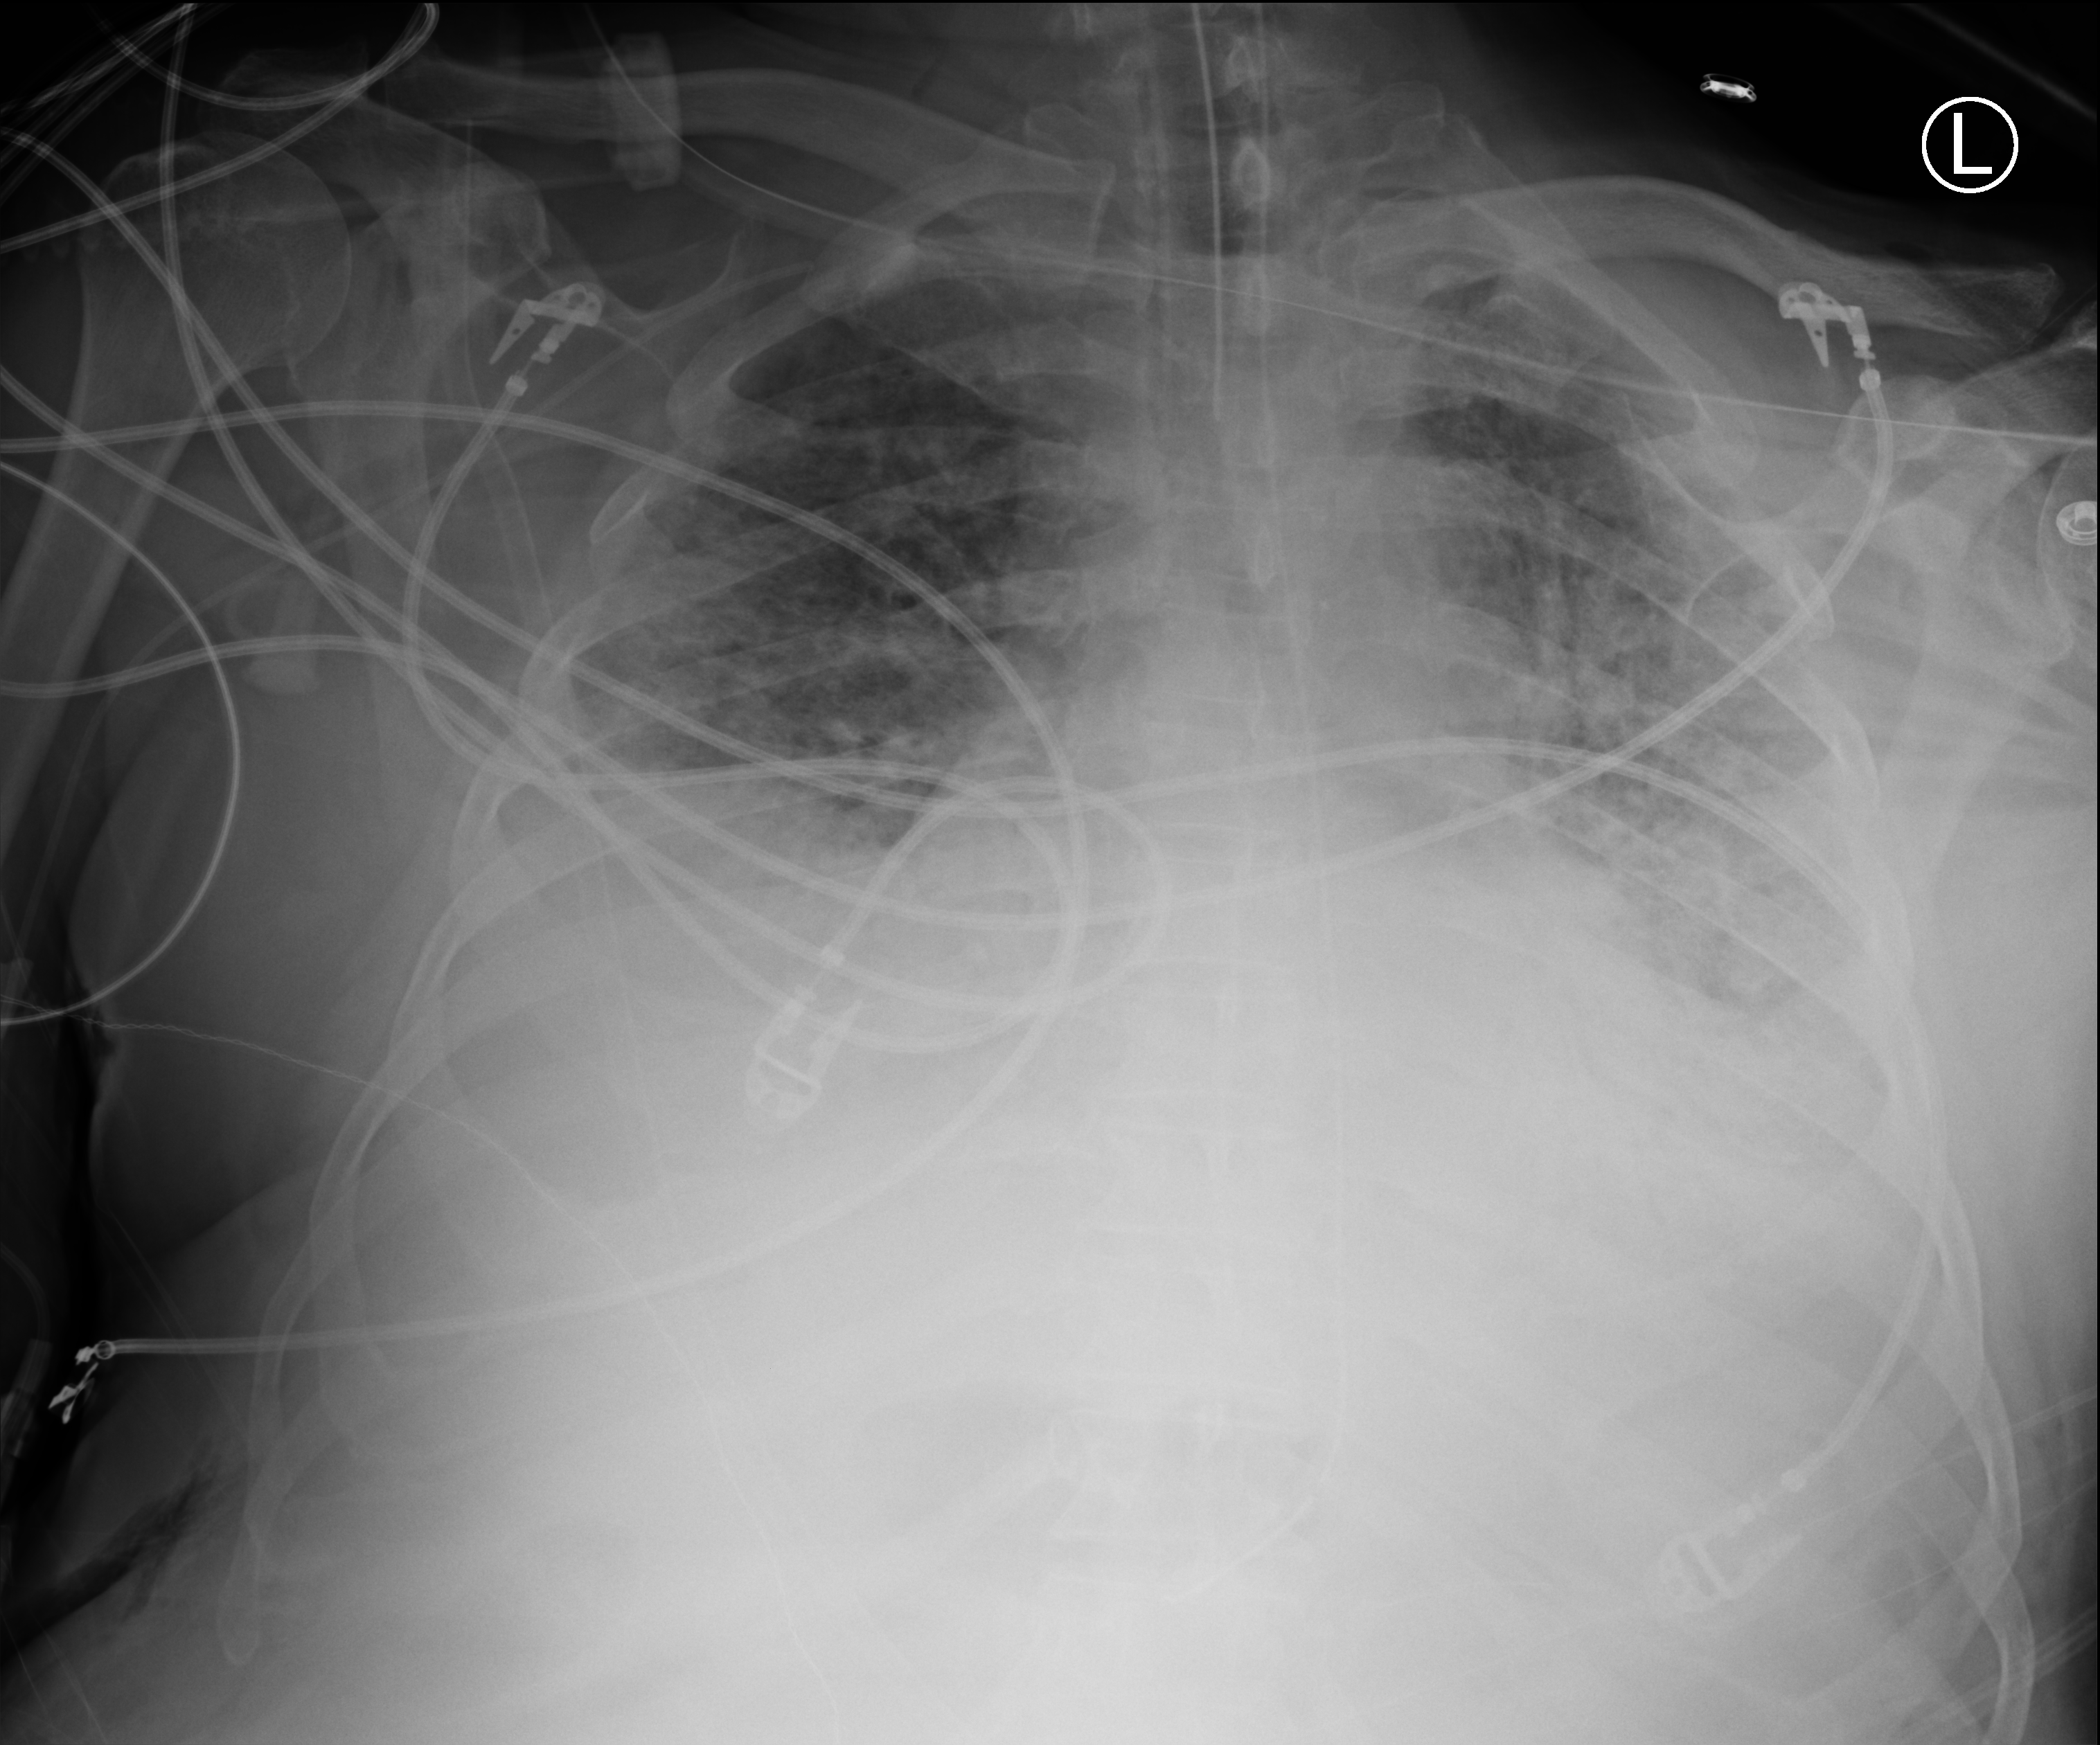
Portable chest radiograph, anteroposterior (AP) projection. Male patient hospitalised with COVID-19, age 60–74 years.
From the hospital-stay record, not from the radiograph (when in the stay this image was taken is not recorded):
- admitted to intensive care during this hospital stay: yes
- hypertension (admission record): yes